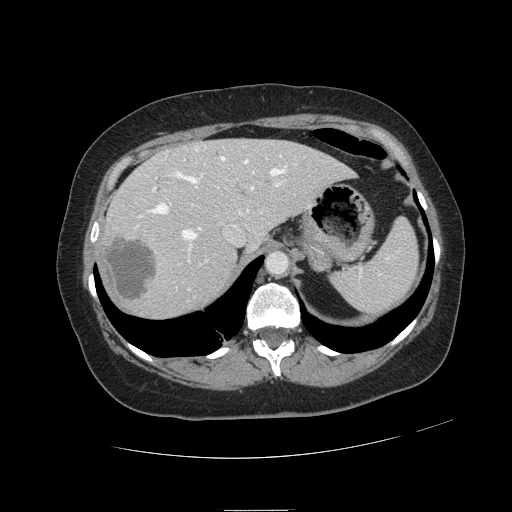
Contrast-enhanced abdominal CT, one axial slice; position 85 of 121 along the scan axis; 120 kVp; intravenous contrast given; soft-tissue window (W 400 / L 40 HU); 2.5 mm slice thickness; 512 × 512 image matrix, field of view 400 × 400 mm. Female patient, age 52 years. Case-level facts recorded for this patient, not image findings: diagnosis: colorectal cancer liver metastases, imaged before liver resection; multiple liver metastases: yes; largest metastasis: 6.3 cm.
Structures marked on this image (expert manual segmentation):
- hepatic veins: bounding box (x1, y1, x2, y2) in pixels: (139, 148, 295, 239)
- liver: (102, 139, 350, 316)
- planned liver remnant (the part of the liver to remain after resection): (168, 139, 351, 246)
- portal vein (with intrahepatic branches): (153, 158, 284, 291)
- liver metastasis: (106, 235, 157, 303)